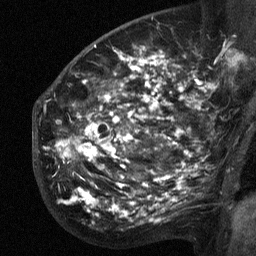
Breast MRI (dynamic contrast-enhanced), one sagittal slice; position 38 of 64 along the scan axis; dynamic contrast-enhanced study with each time point stored as its own series, time point 2 of 3 at this slice position (early post-contrast, ordered by acquisition time); 1.5 T; TE 4.8 ms, TR 27 ms; 2.3 mm slice thickness; 256 × 256 image matrix, field of view 200 × 200 mm. Female patient, age 50 years. From the clinical record (not read from this slice): setting: breast cancer imaged before/during neoadjuvant chemotherapy; receptor status: HER2-positive.
Annotated regions visible in this slice (semi-automatic segmentation, software-assisted and operator-edited):
- analysis volume of interest (the breast-tissue region the enhancement analysis was run in; not a lesion): bounding box <53,64,211,217> (left, top, right, bottom; pixels)
- tumour enhancement mask (voxels above the 90 % enhancement threshold inside the analysis volume of interest): <57,64,181,212>